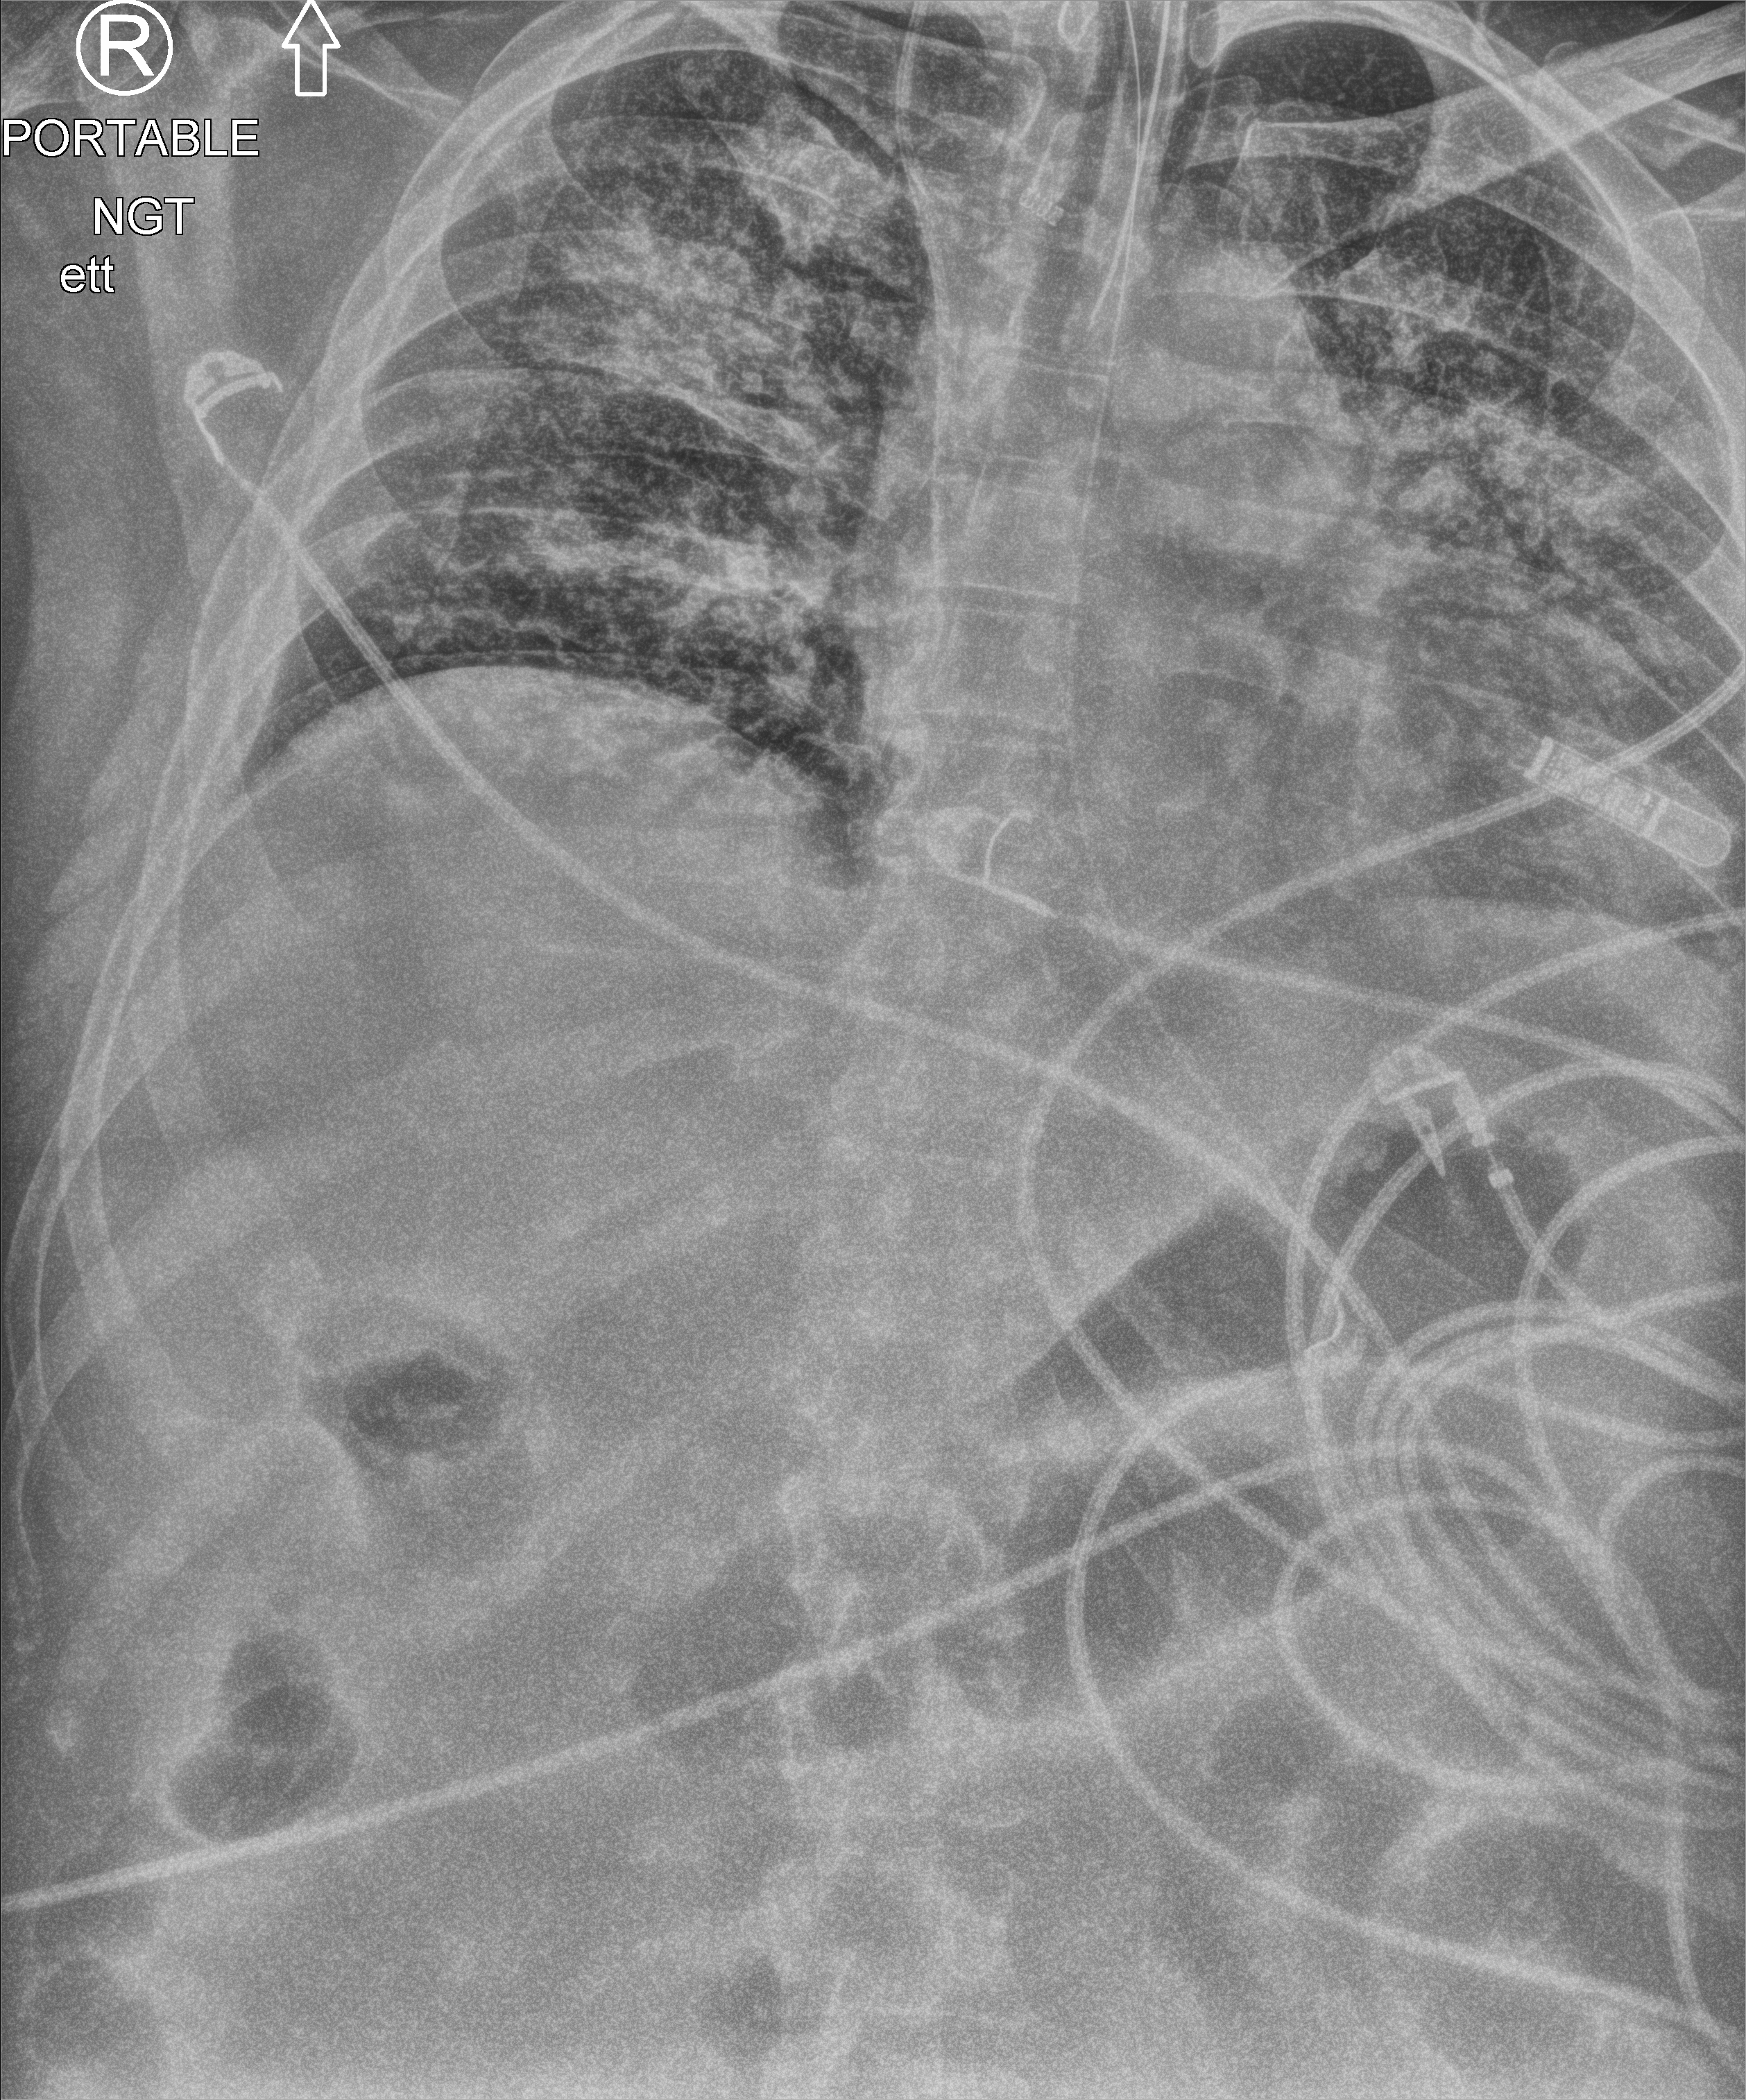
Chest X-ray (portable). Patient hospitalised with COVID-19; male, aged 18–59 years.
From the hospital-stay record, not from the radiograph (when in the stay this image was taken is not recorded): admitted to intensive care during this hospital stay: yes; mechanically ventilated during this hospital stay: yes.